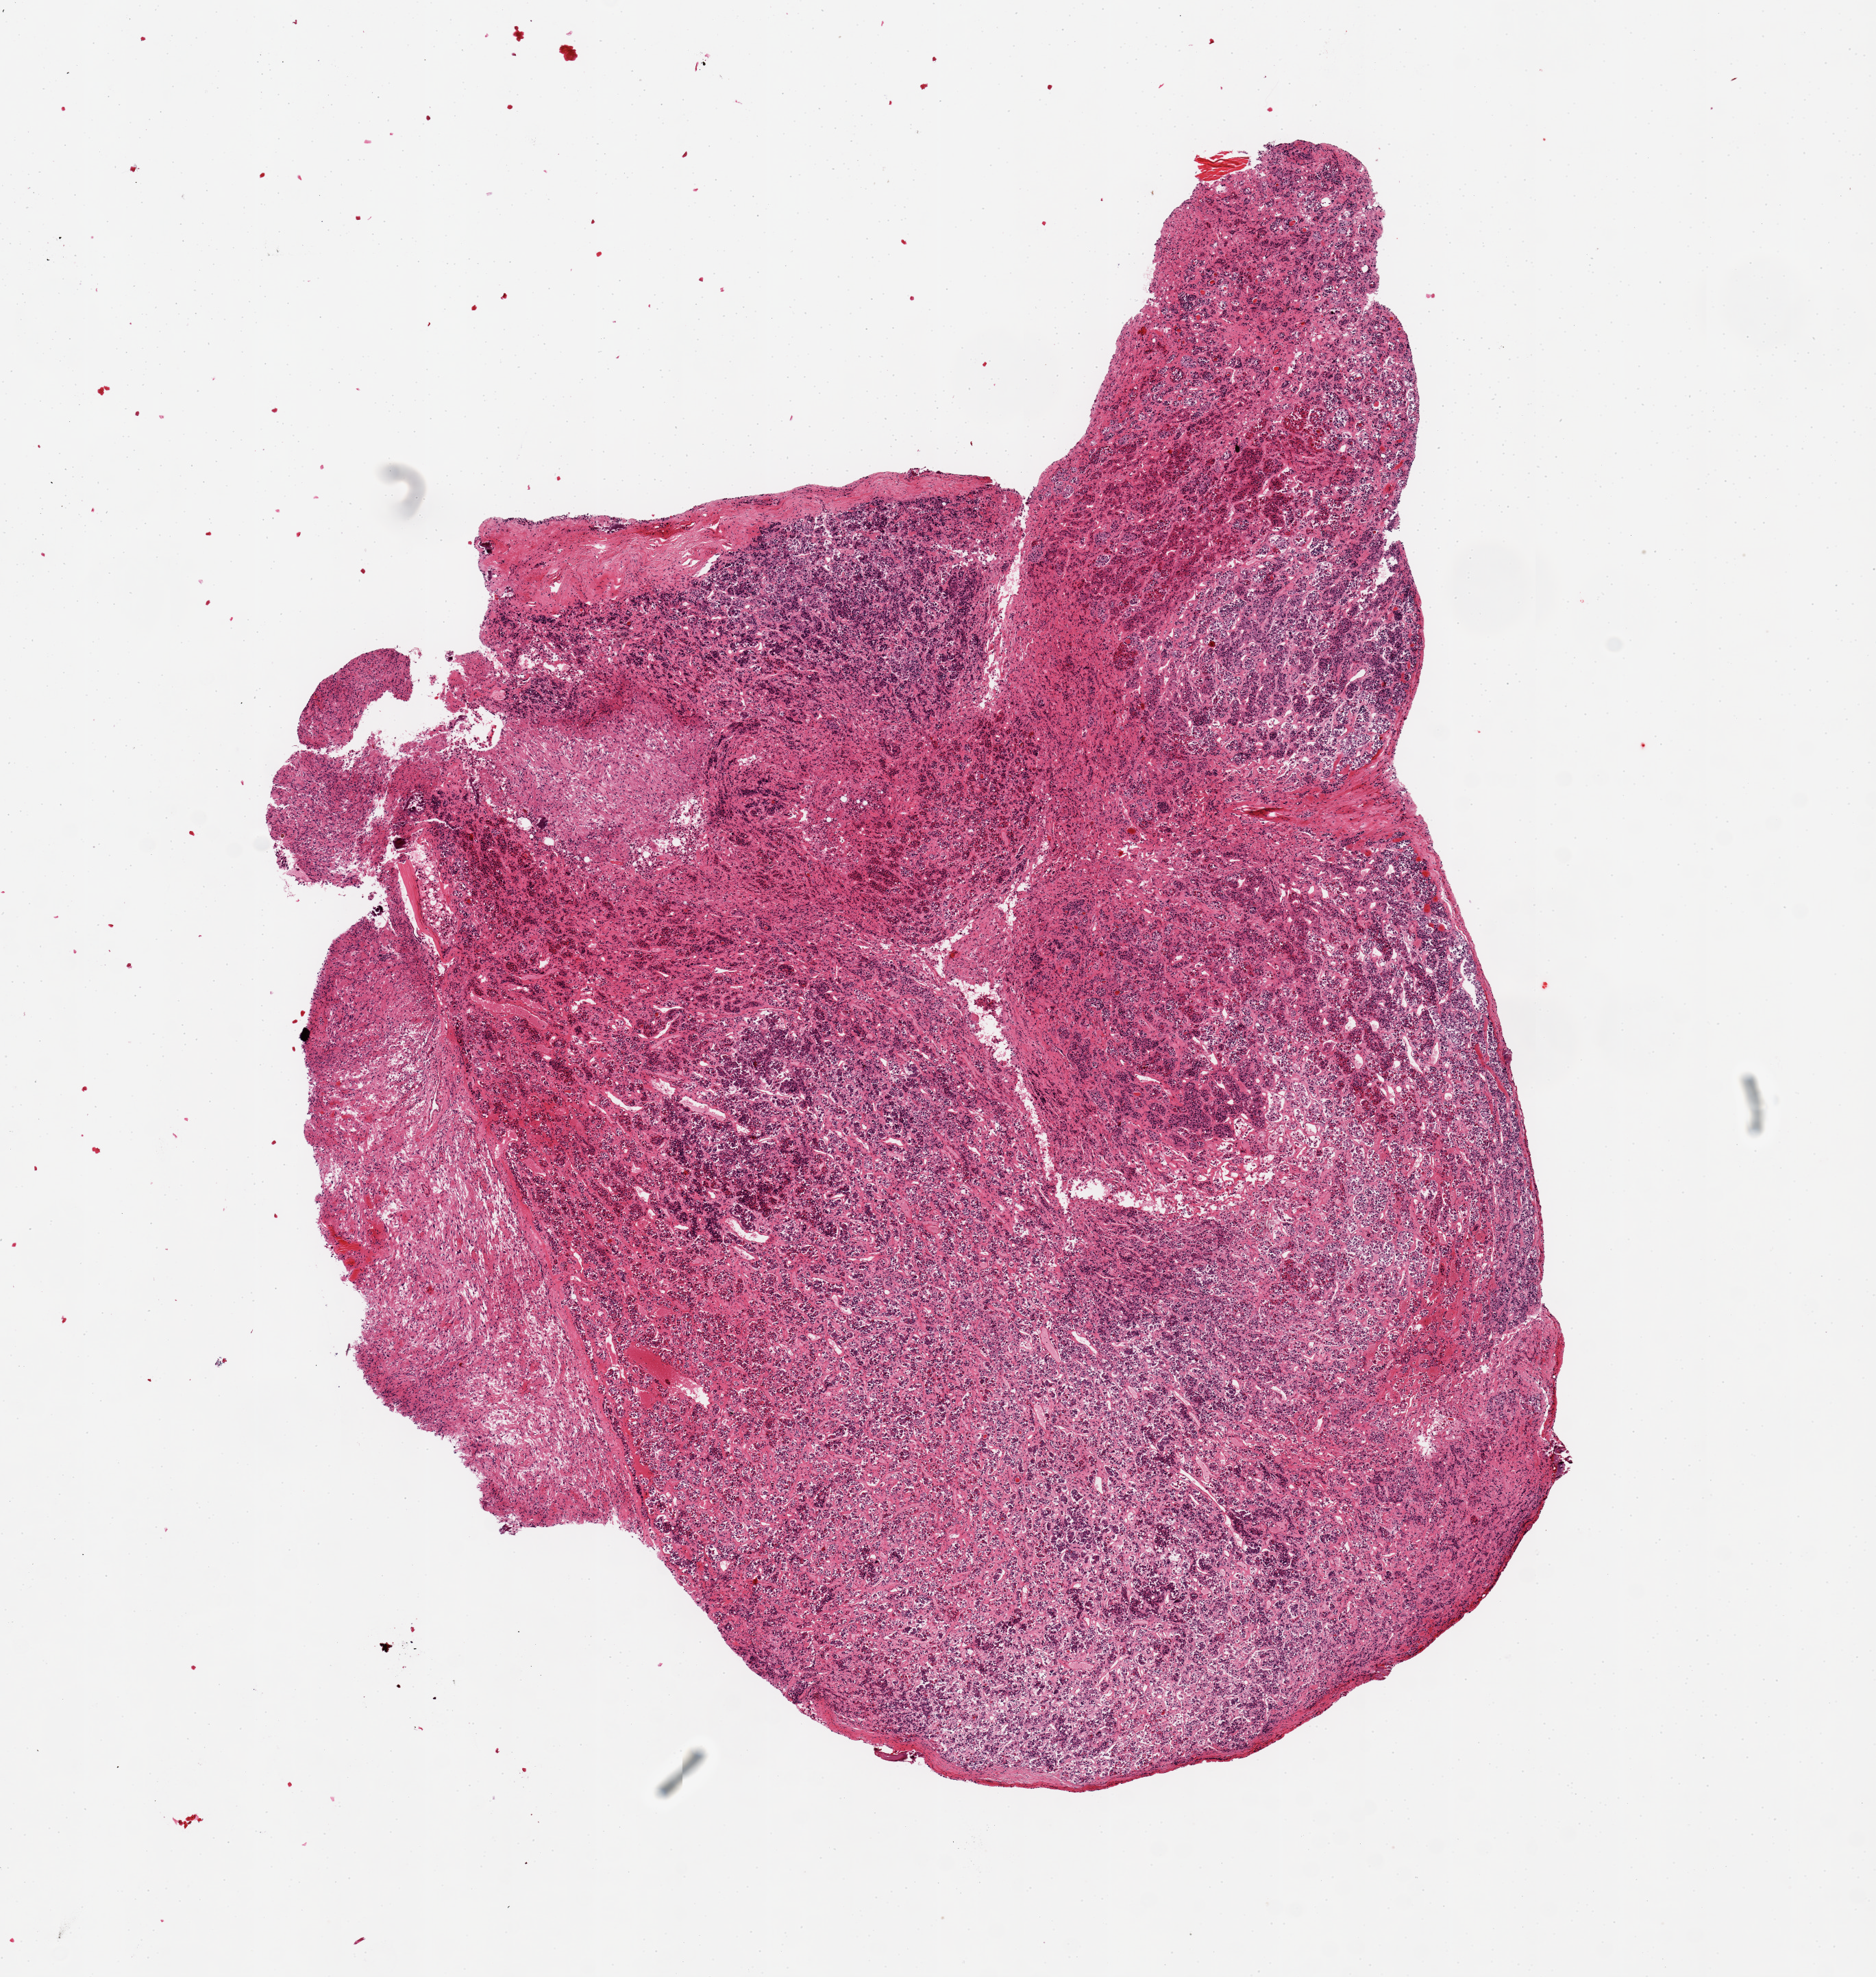
Digitized haematoxylin and eosin-stained section, brightfield — low-resolution overview of the scanned area, about 10.8 x 11.4 mm; PAXgene-fixed, paraffin-embedded tissue; section of pituitary (target tissue); tissue donor sample.
- pathologist's review note for this sample: 1 aliquot, ~8x7mm. Badly autolyzed